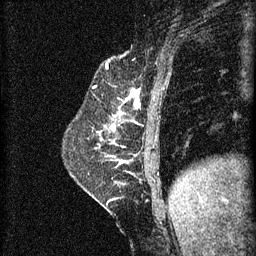
Breast MRI (dynamic contrast-enhanced), one sagittal slice. Slice 19 of 60 in the series (ordered by position). 3 images stored at this slice position (order not interpretable as contrast timing). 1.5 T. TE 4.2 ms, TR 8.2 ms. 2 mm slice thickness. 256 × 256 image matrix. Patient: female, 59 years.
Structures marked on this image (semi-automatic segmentation, software-assisted and operator-edited):
- analysis volume of interest (the breast-tissue region the enhancement analysis was run in; not a lesion): bounding box [x1, y1, x2, y2] px = [98, 92, 137, 135]
- tumour enhancement mask (voxels above the 70 % enhancement threshold inside the analysis volume of interest): [124, 92, 137, 103]